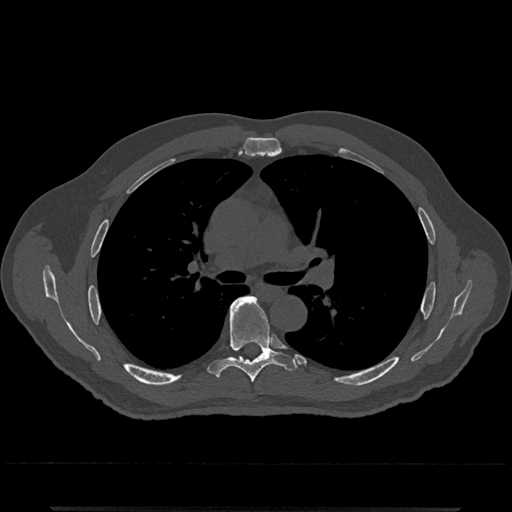
CT including the spine, one axial slice; slice 776 of 797 in the series (ordered by position); 120 kVp; bone window (W 1800 / L 400 HU); 512 × 512 image matrix. Patient: male, 67 years. Case-level facts recorded for this patient, not image findings: primary cancer: prostate.
Annotated regions visible in this slice (semi-automatically segmented with operator editing):
- T6 vertebra: bounding box (x1, y1, x2, y2) in pixels: (207, 296, 297, 383)